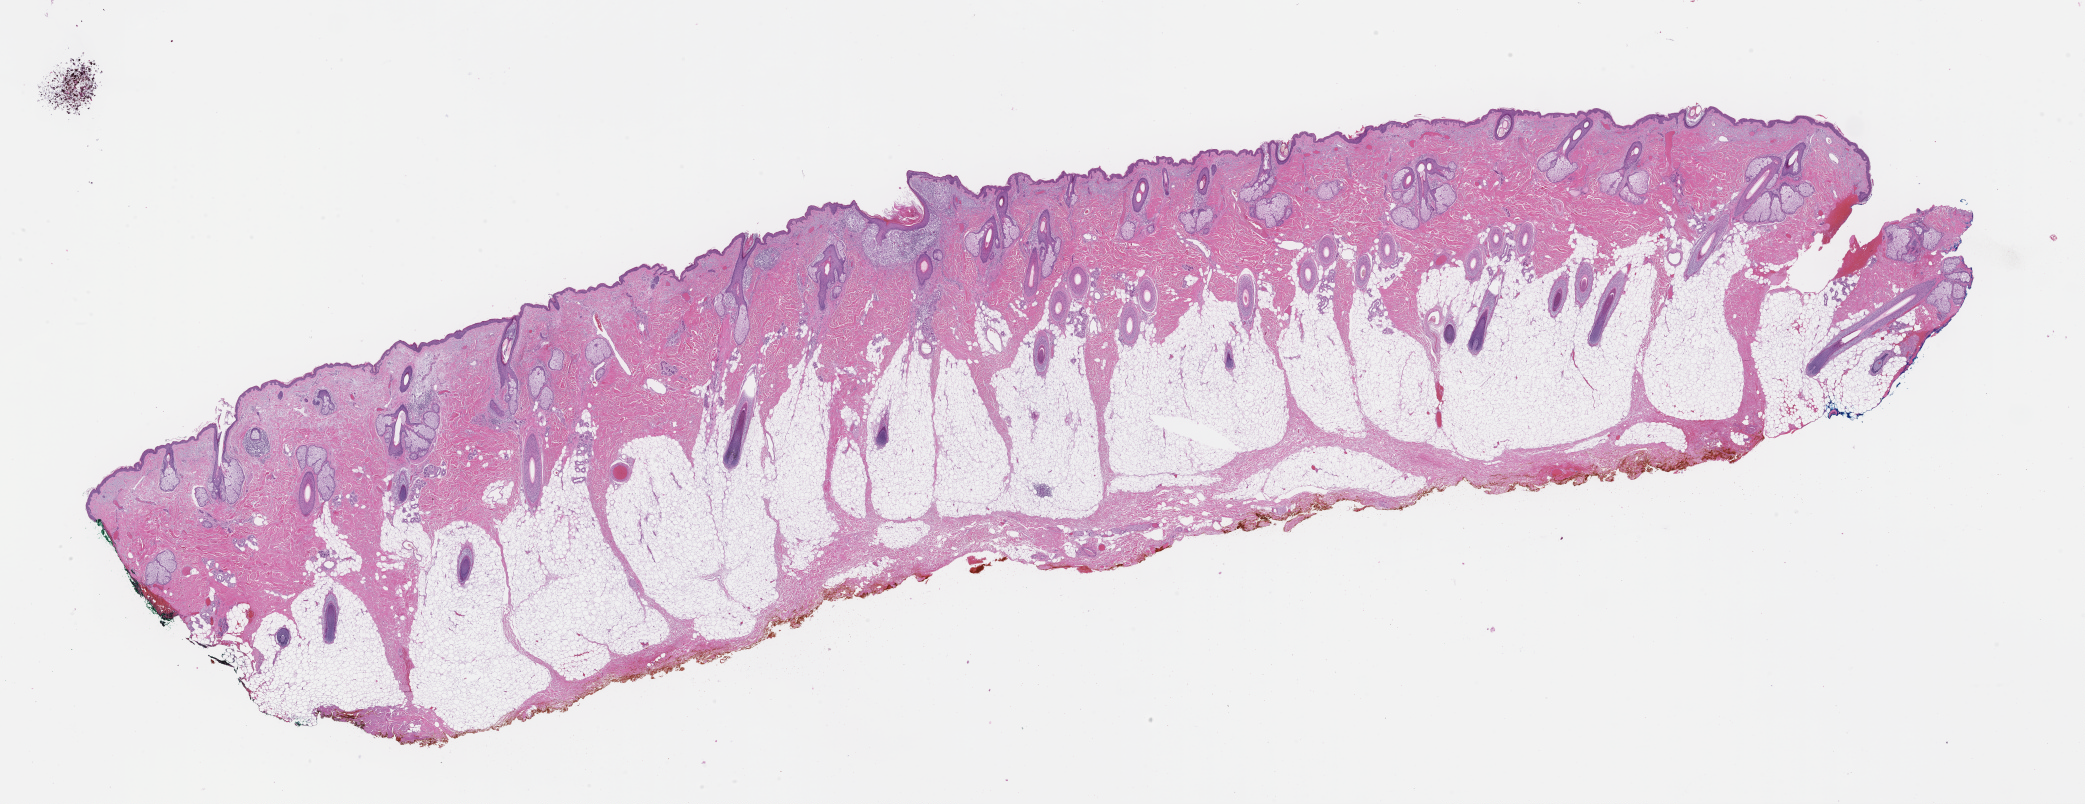
H&E whole-slide image, whole scanned area (about 33.7 x 13.0 mm) shown as a low-resolution overview; formalin-fixed paraffin-embedded section; site: skin; archival tissue. Male patient.
This section: primary tumor. Diagnosis: Melanoma.